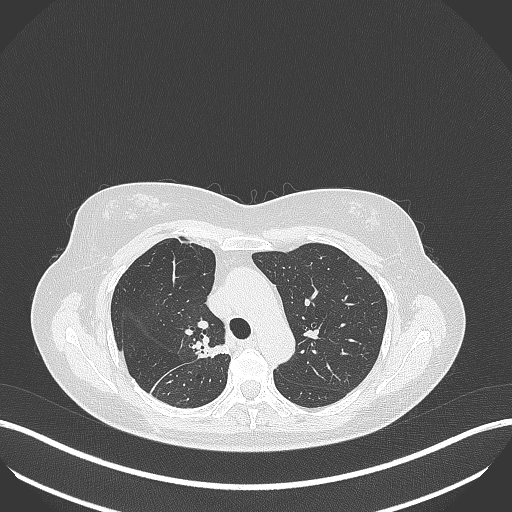
Chest CT, one axial slice. Position 276 of 386 along the scan axis. 120 kVp. Lung window (W 1500 / L -600 HU). 1 mm slice thickness. 512 × 512 image matrix. Patient: female, 65 years. Case-level facts recorded for this patient, not image findings: clinical TNM (as recorded): T1b N0 M0; histopathological grade: G2.
Outlined on this slice (rectangle marked by the reading radiologist):
- lung tumour (recorded histology: adenocarcinoma): box from (x=189, y=338) to (x=228, y=362) px